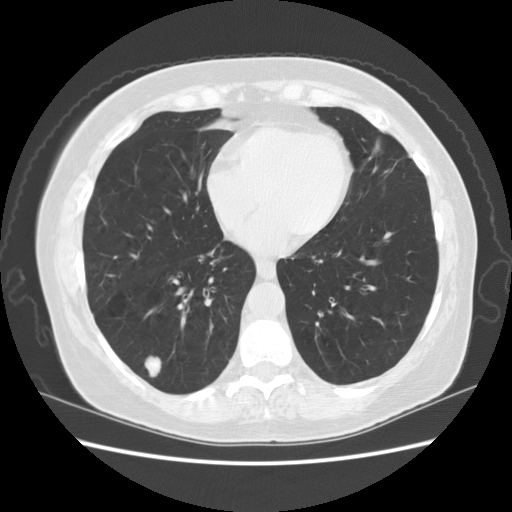
Axial slice from a low-dose chest CT screening exam; third screening round (two years after baseline); lung window (W 1500 / L -600 HU); 2.5 mm slice thickness; standard (soft-tissue) reconstruction kernel (STANDARD); 120 kVp; slice 106 of 156 in the series. Female, age 59 years at enrolment. Current smoker at enrolment.
• Expert reader's lesion annotation, bounding box [x1, y1, x2, y2] px = [133, 349, 171, 385].
• Screening reader's record for this exam (one nodule recorded; not confirmed to be the boxed lesion): non-calcified nodule or mass ≥4 mm, right lower lobe, 16 × 11 mm, smooth margins, soft tissue attenuation, pre-existing on the prior screen: yes; interval growth: yes.